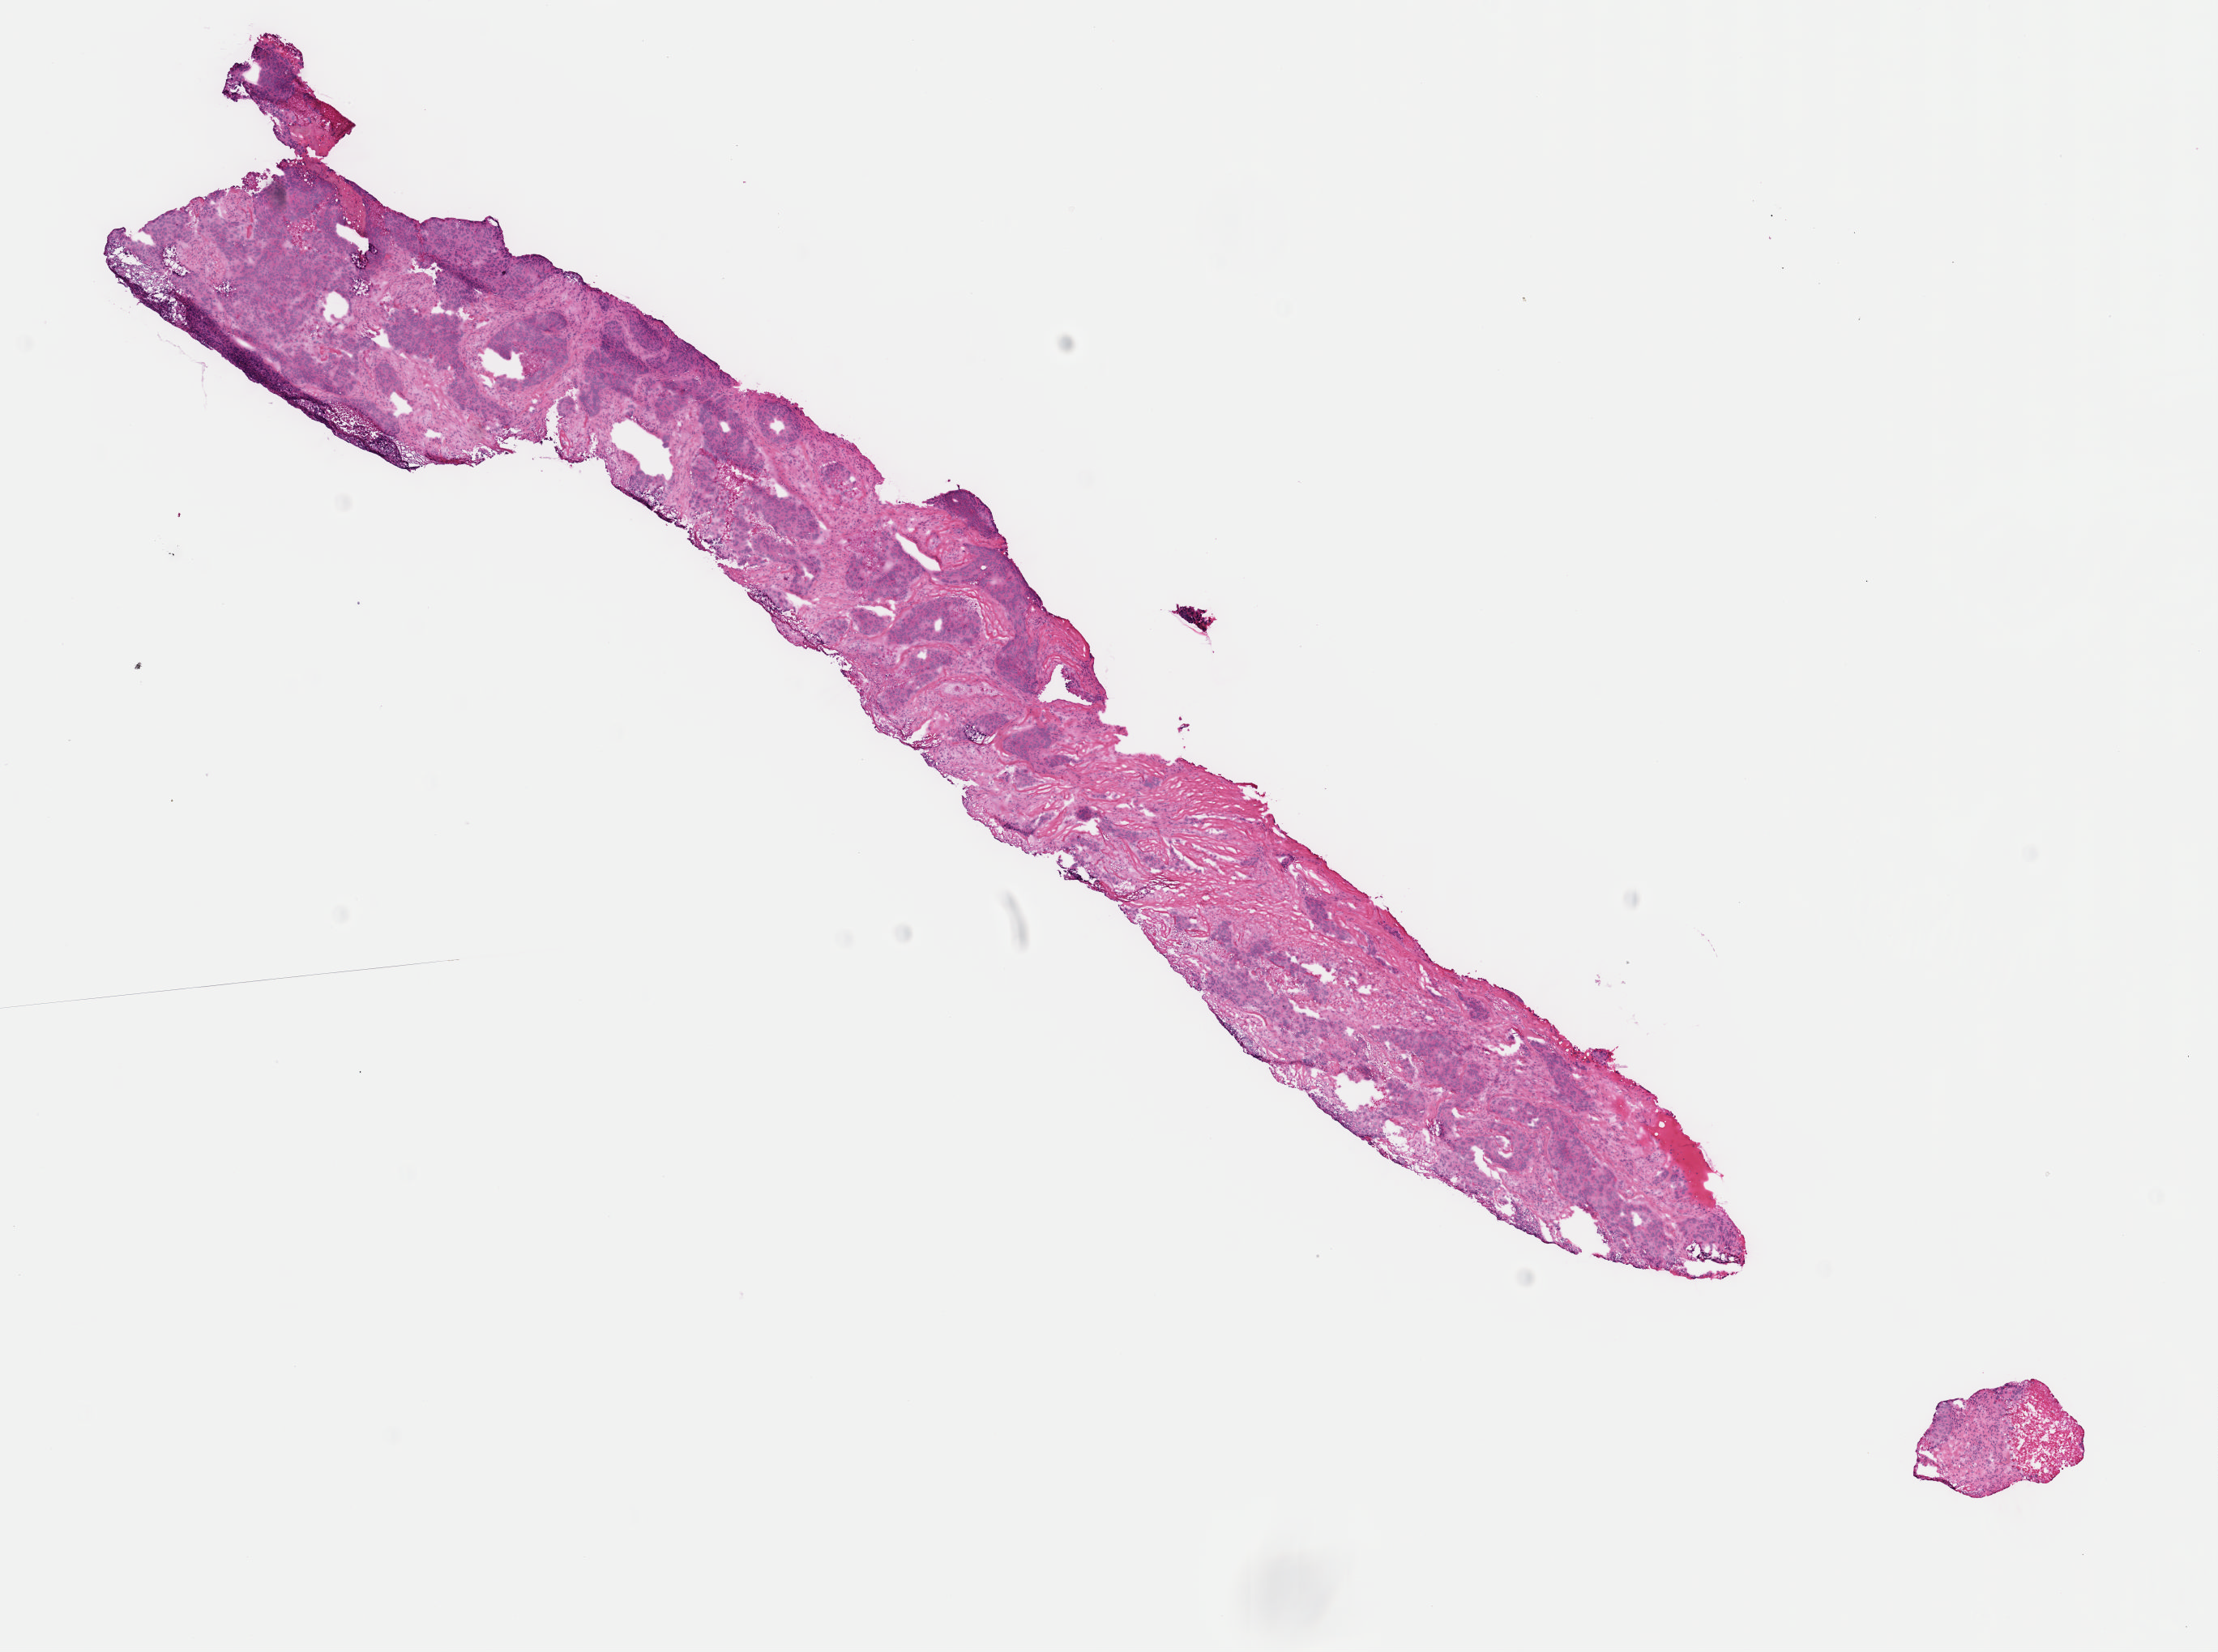
Whole-slide histology image, H&E-stained — whole scanned area (about 10.8 x 8.1 mm) shown as a low-resolution overview, frozen section from the top of the tissue portion, primary tumour sample from the breast. Female, age 47 years at initial diagnosis. Composition of this section per pathologist review: tumour cells 100%, tumour nuclei 90%, normal cells 0%, stromal cells 0%, necrosis 0%. Inflammatory infiltration, as recorded: lymphocyte infiltration 0%, monocyte infiltration 0%, neutrophil infiltration 0%.
AJCC pathologic stage: I (6th edition). Laterality: right. Histologic diagnosis: Infiltrating duct carcinoma, NOS.